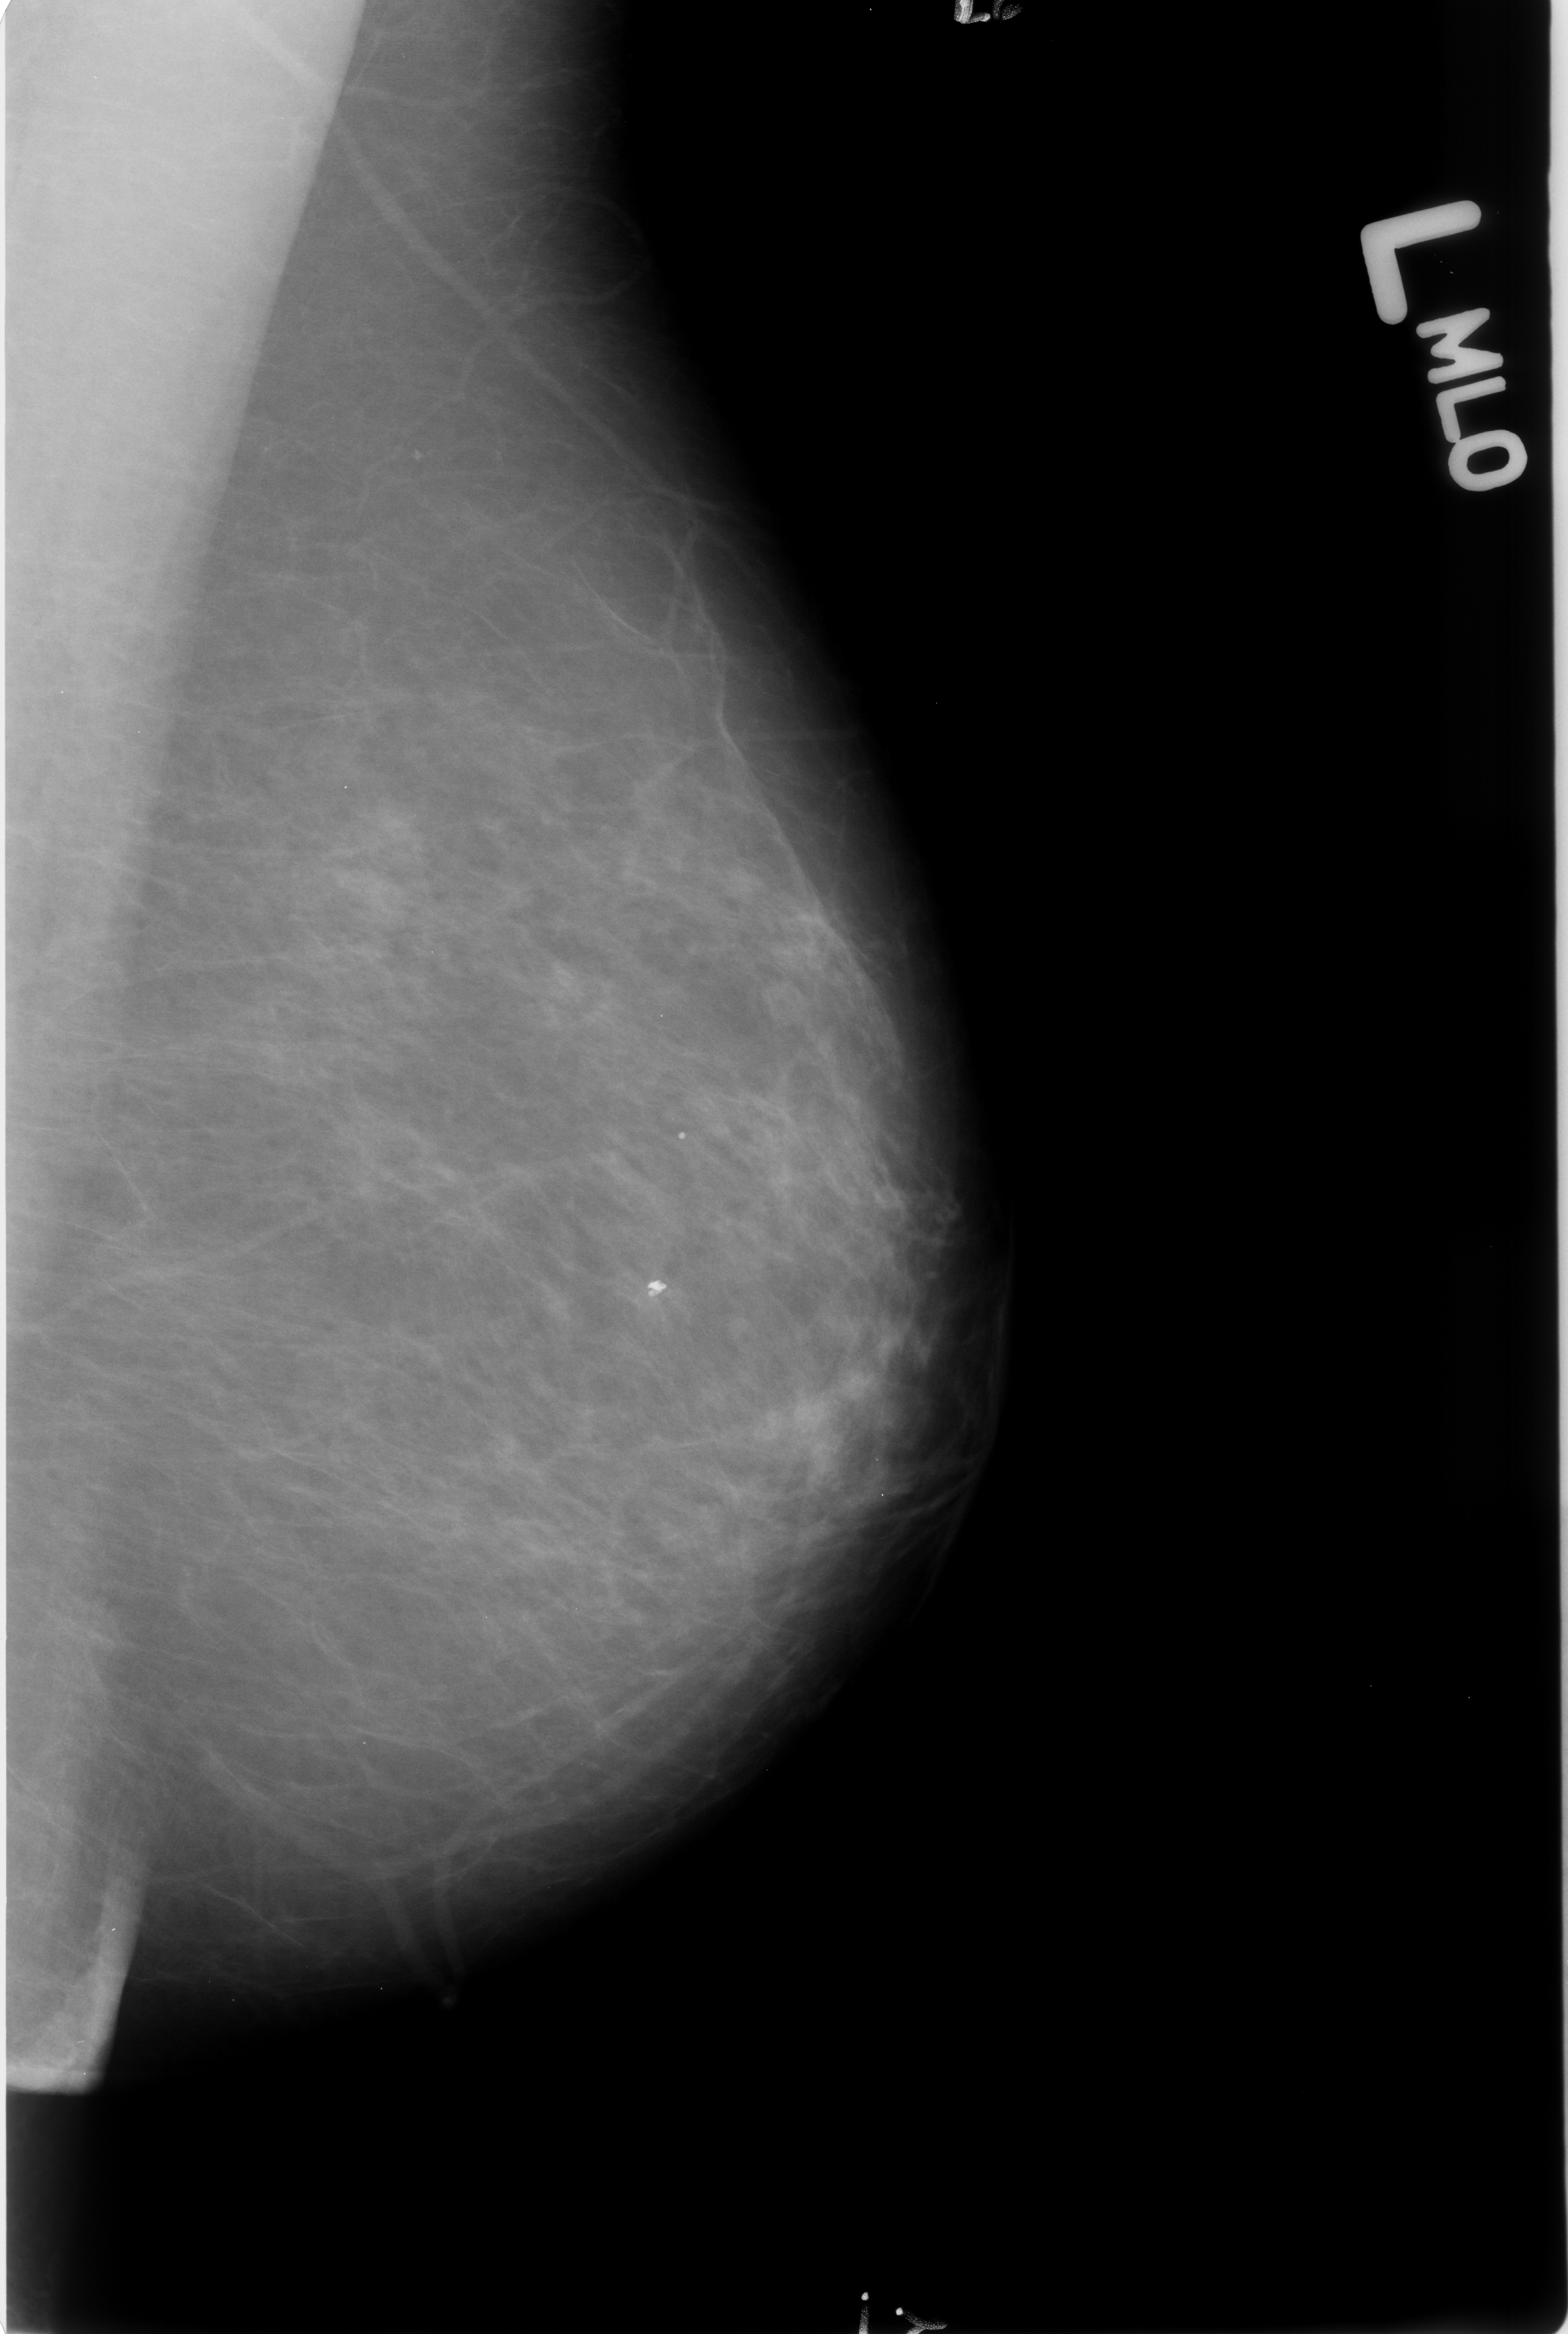
Scanned film-screen mammogram; left breast; MLO view; BI-RADS breast density category 1 (scale 1–4).
Calcifications, morphology coarse; BI-RADS assessment category 2; benign; no additional work-up was recommended (benign without callback).